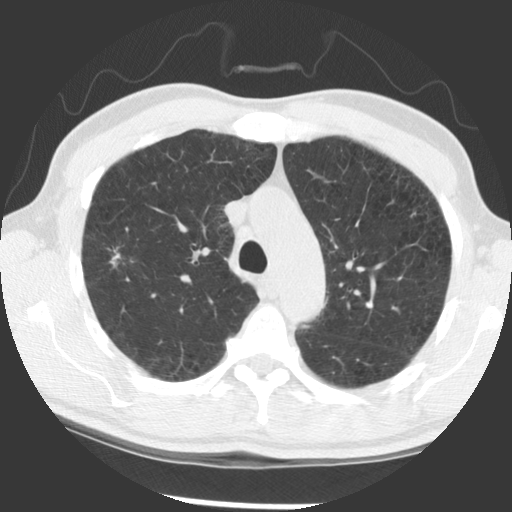
Chest CT (low-dose screening protocol), one axial image; baseline screening round; lung window (W 1500 / L -600 HU); 512 × 512 image matrix. Male participant, aged 56 years at enrolment. Current smoker at enrolment.
Lesion marked by an expert reader, bounding box [x1, y1, x2, y2] px = [73, 231, 144, 290]. Reader record for this screening exam (exam-level; its link to the box is not recorded): non-calcified nodule or mass ≥4 mm, right upper lobe, 12 × 7 mm, spiculated (stellate) margins, soft tissue attenuation. Official screen result: positive, change unspecified: nodule(s) >= 4 mm or enlarging nodule(s), mass(es), or other non-specific abnormalities suspicious for lung cancer. Later outcome: lung cancer diagnosed 676 days after this screen (after the second annual screen) — squamous cell carcinoma, NOS, right upper lobe, right middle lobe, moderately differentiated (G2), stage IB (AJCC 6th edition), 70 mm at pathology.